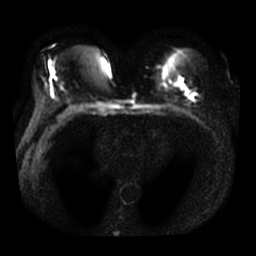
Breast MRI, one axial slice; diffusion-weighted series; image 2 of 4 stored at this slice position (different b-values; order by instance number); 3 T; 5 mm slice thickness; 256 × 256 image matrix, field of view 320 × 320 mm. Female patient.
Outlined on this slice (manually delineated by an expert):
- tumour on diffusion-weighted imaging: bounding box [x1, y1, x2, y2] px = [181, 85, 195, 98]